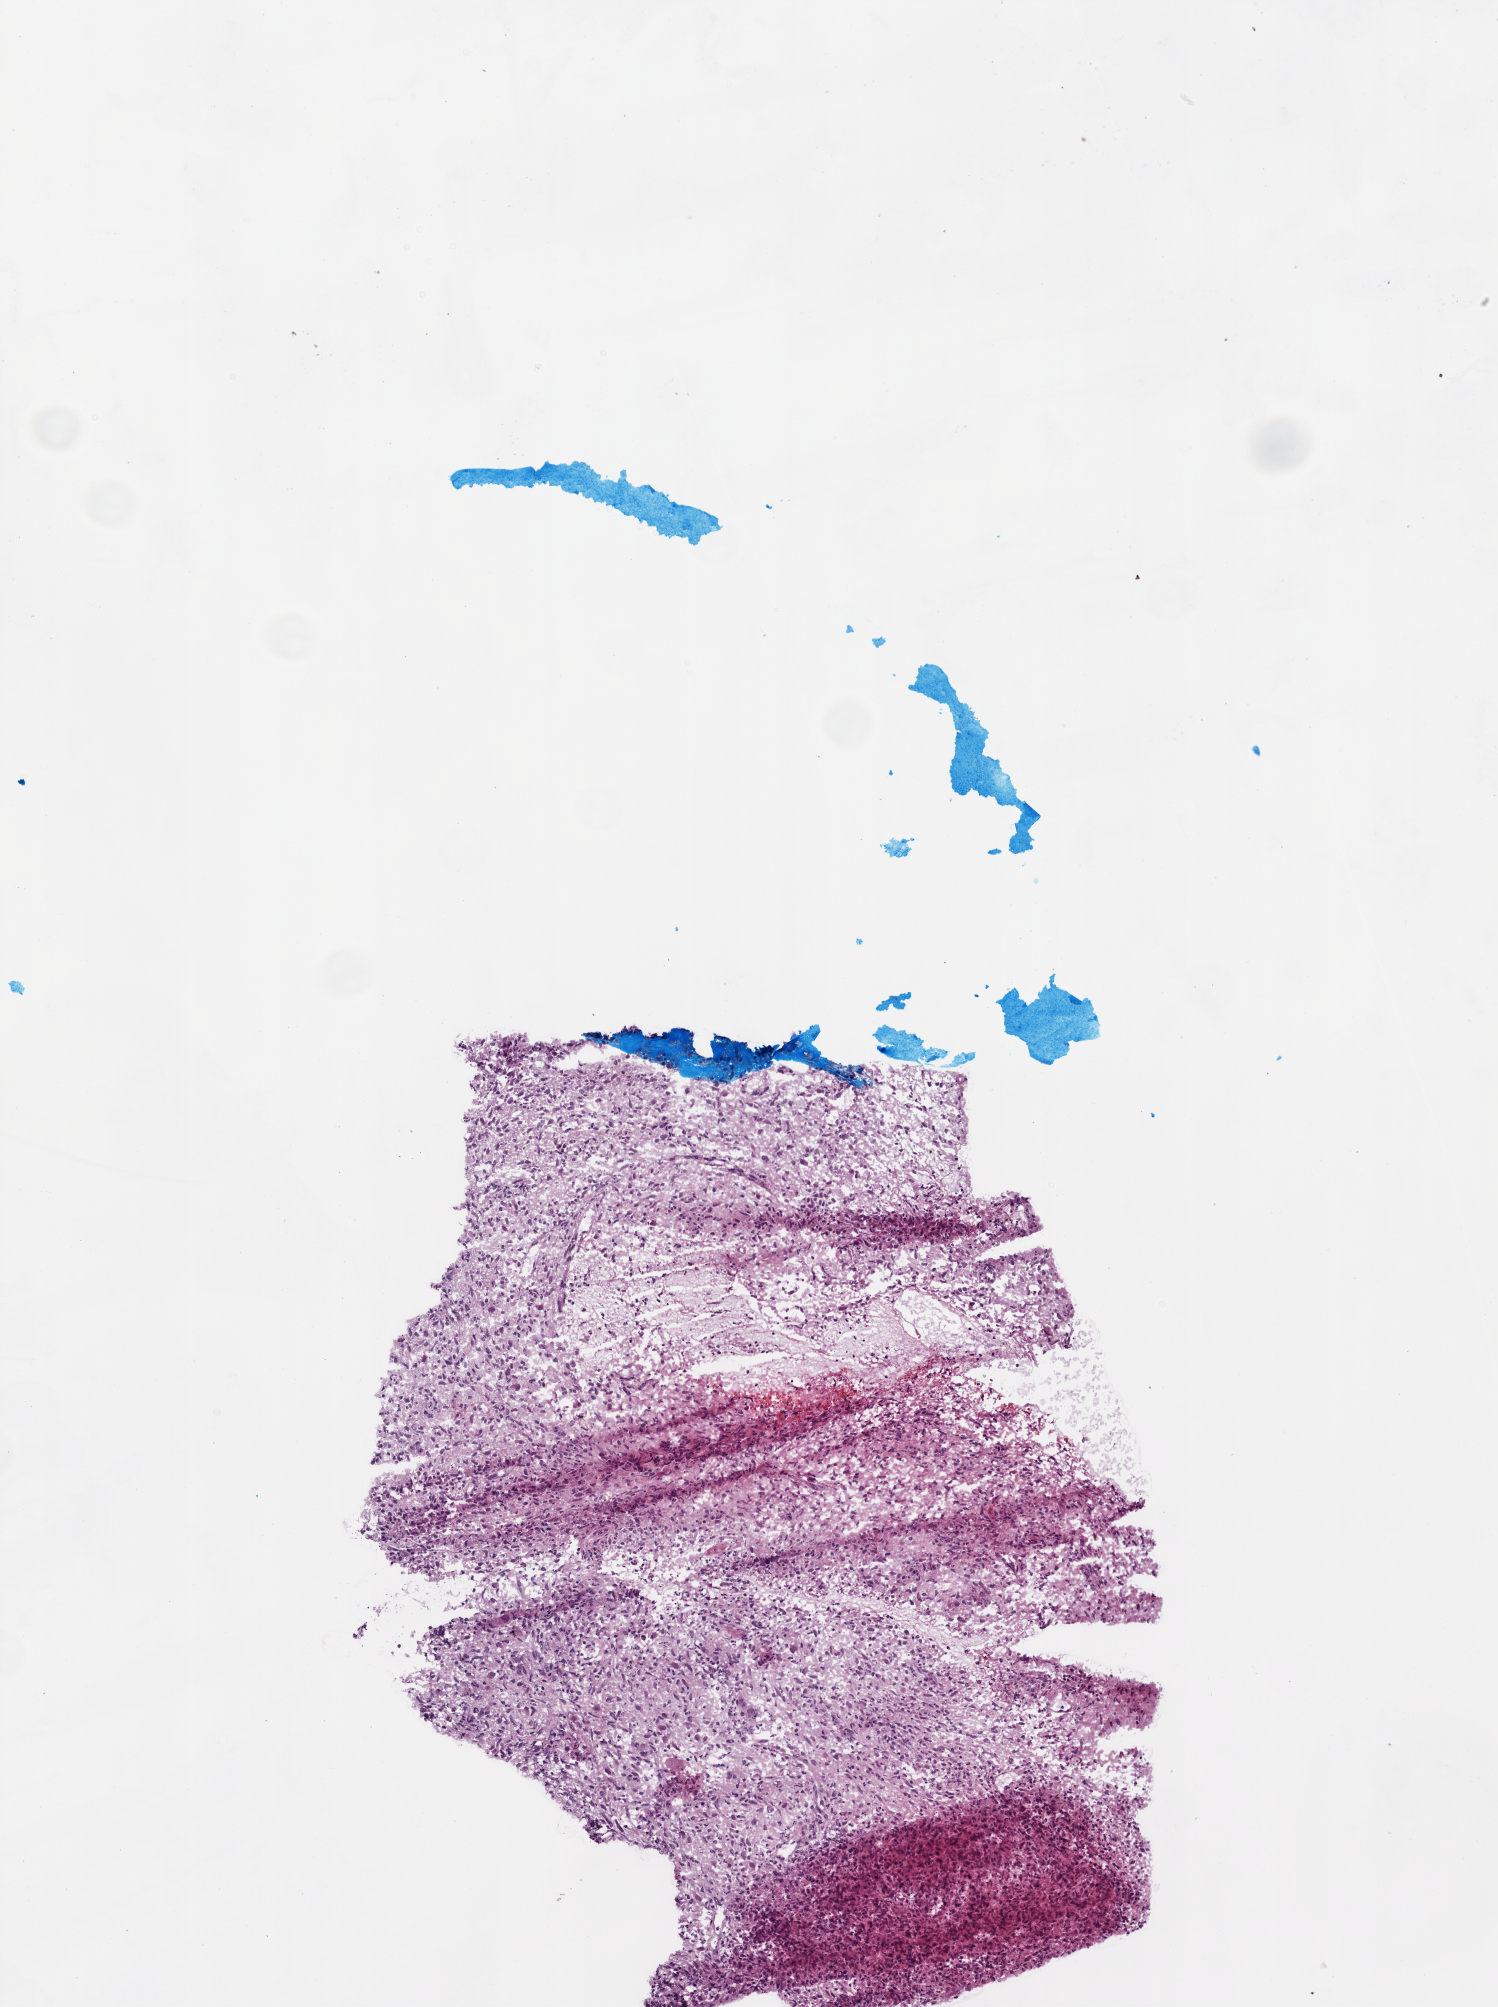
Whole-slide histology image, H&E, shown as a low-resolution overview of the whole scanned area (about 3.0 x 4.0 mm, slide scanned at 20x), frozen section from the top of the tissue portion, brain, primary tumour sample. Male patient; age at initial diagnosis 63 years. Pathologist review of this section (percent, as recorded): tumour cells 90%, tumour nuclei 100%, normal cells 0%, stromal cells 0%, necrosis 10%.
Diagnosis: Glioblastoma.